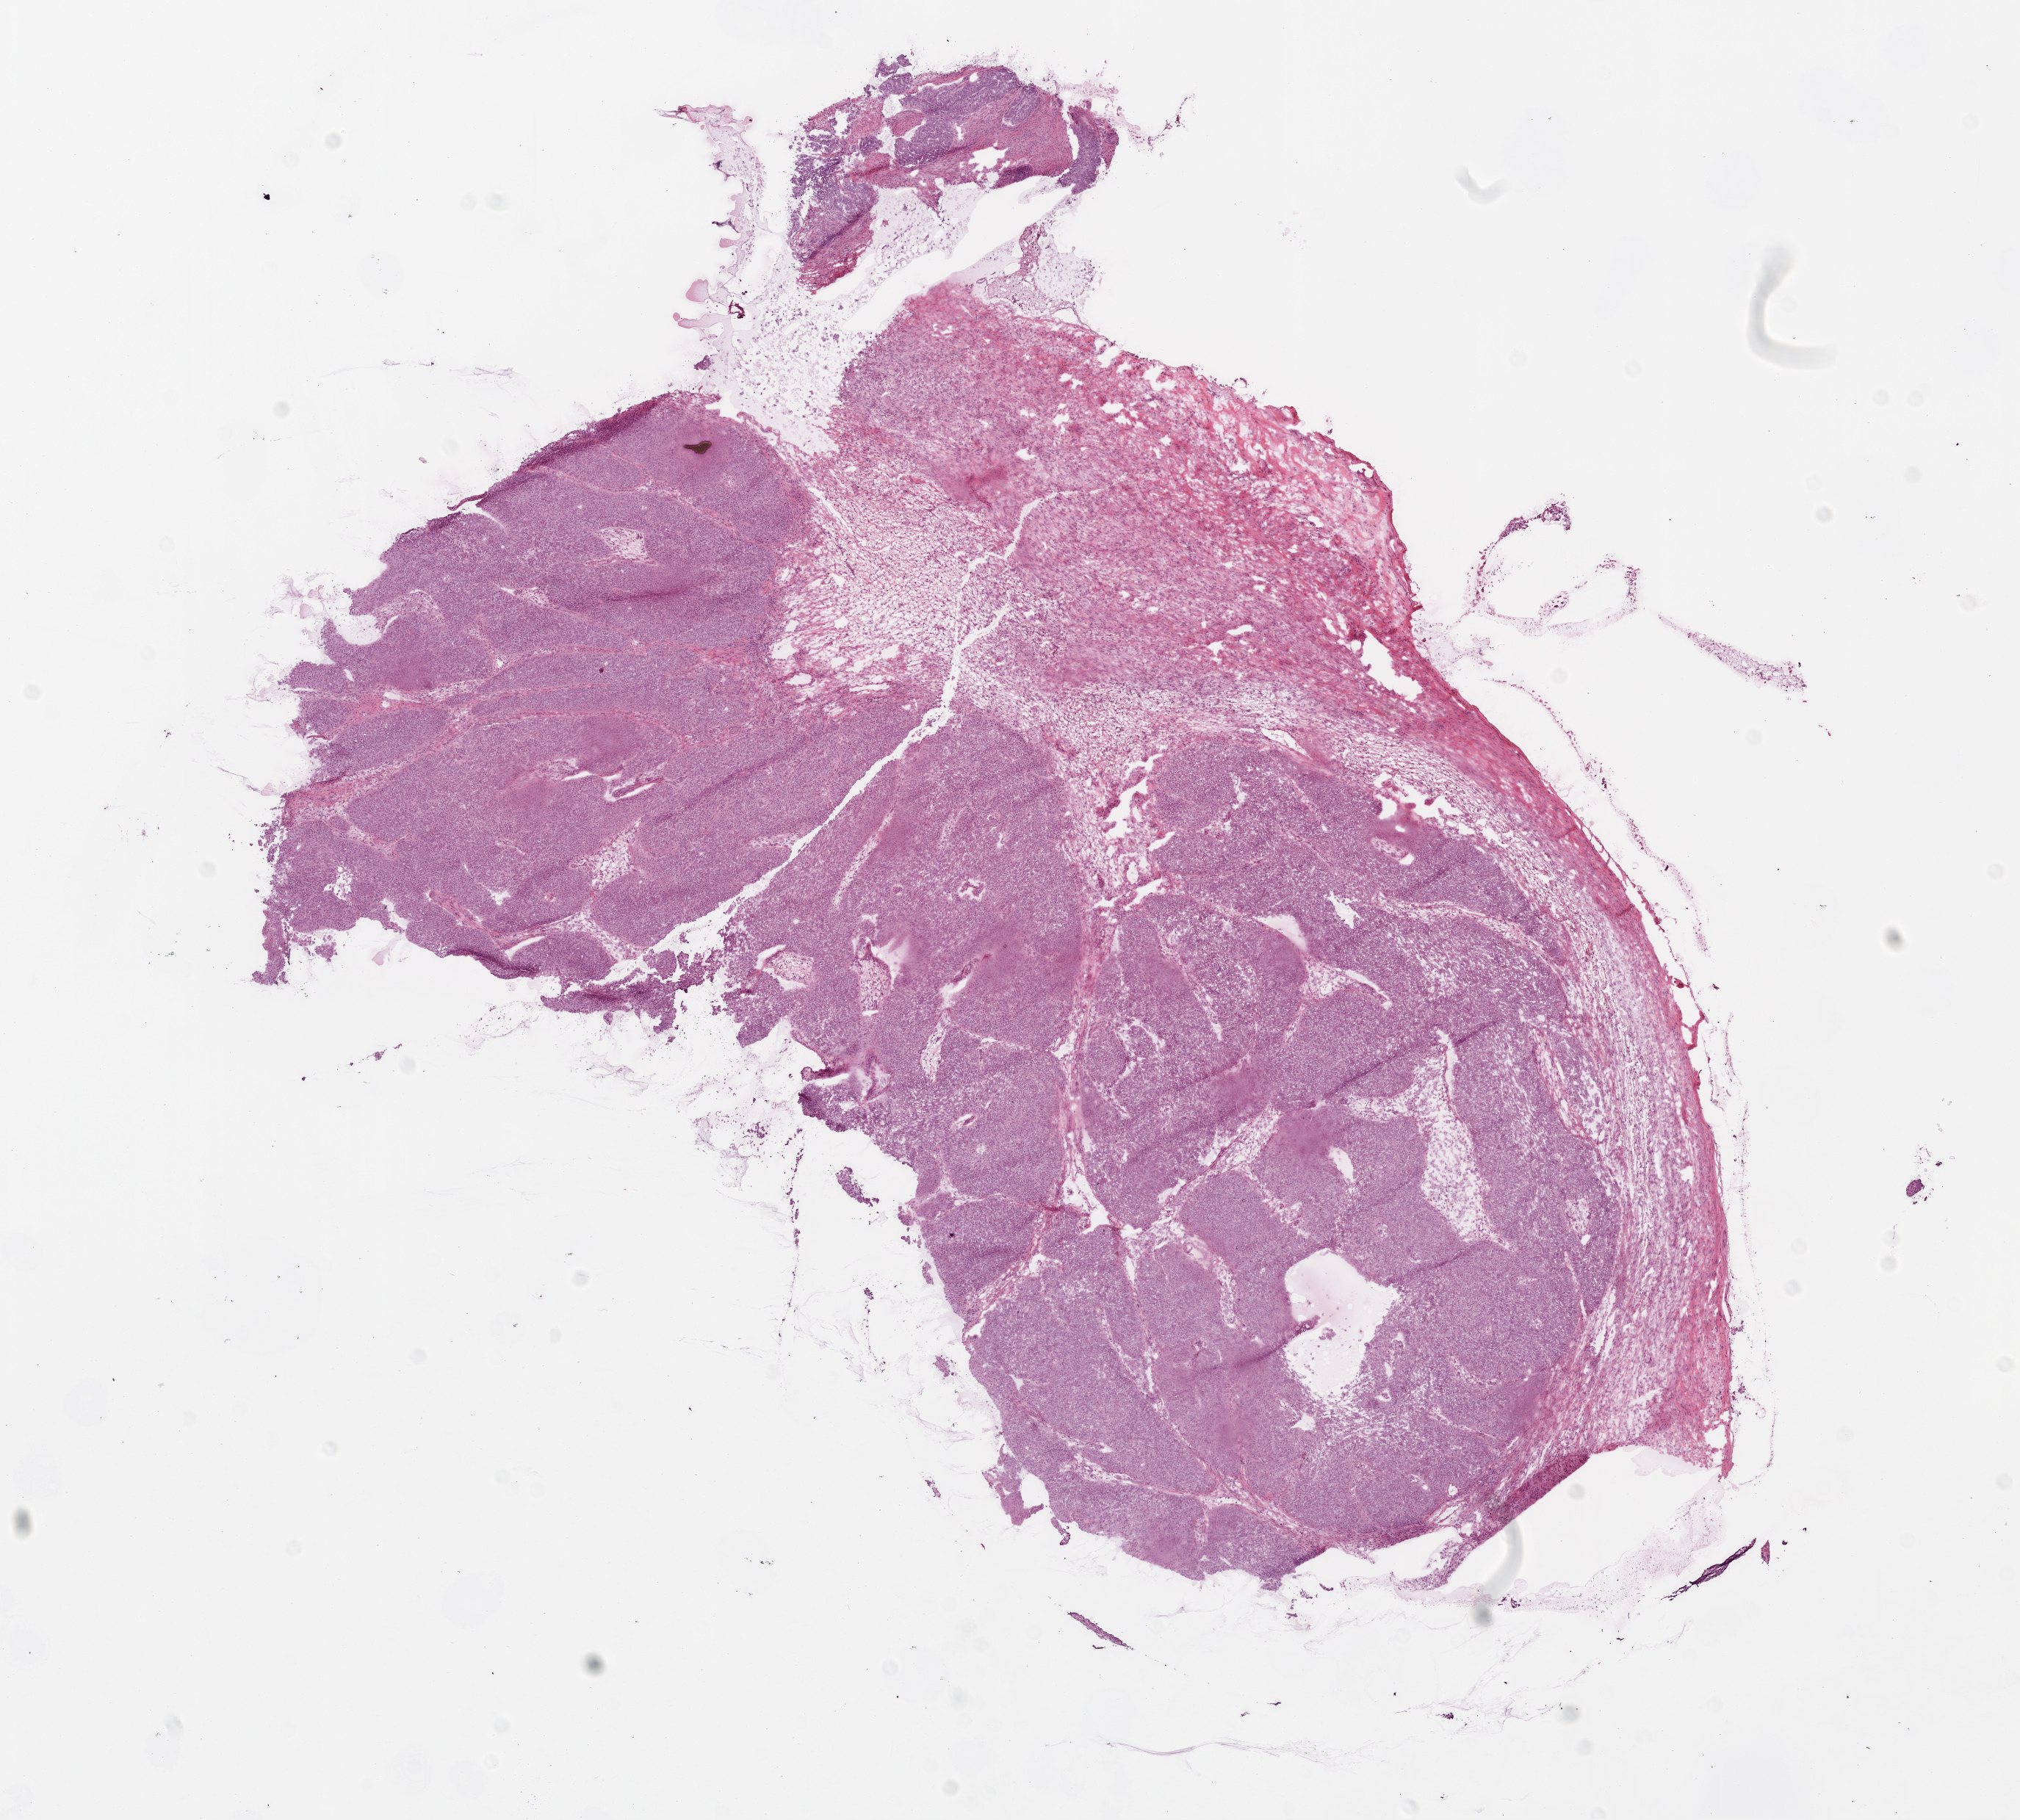
Digitized Hematoxylin and eosin (H&E) stained tissue section (whole slide) — shown as a low-resolution overview of the whole scanned area (about 11.0 x 9.9 mm), frozen section from the top of the tissue portion, primary tumour sample from the ovary. Patient: female, age at initial diagnosis 62 years. Histologic grade: G3 (poorly differentiated). Pathologist review of this section (percent, as recorded): tumour cells 95%, tumour nuclei 95%, normal cells 0%, stromal cells 5%, necrosis 0%.
* FIGO stage: IC
* pathologic diagnosis: Serous cystadenocarcinoma, NOS